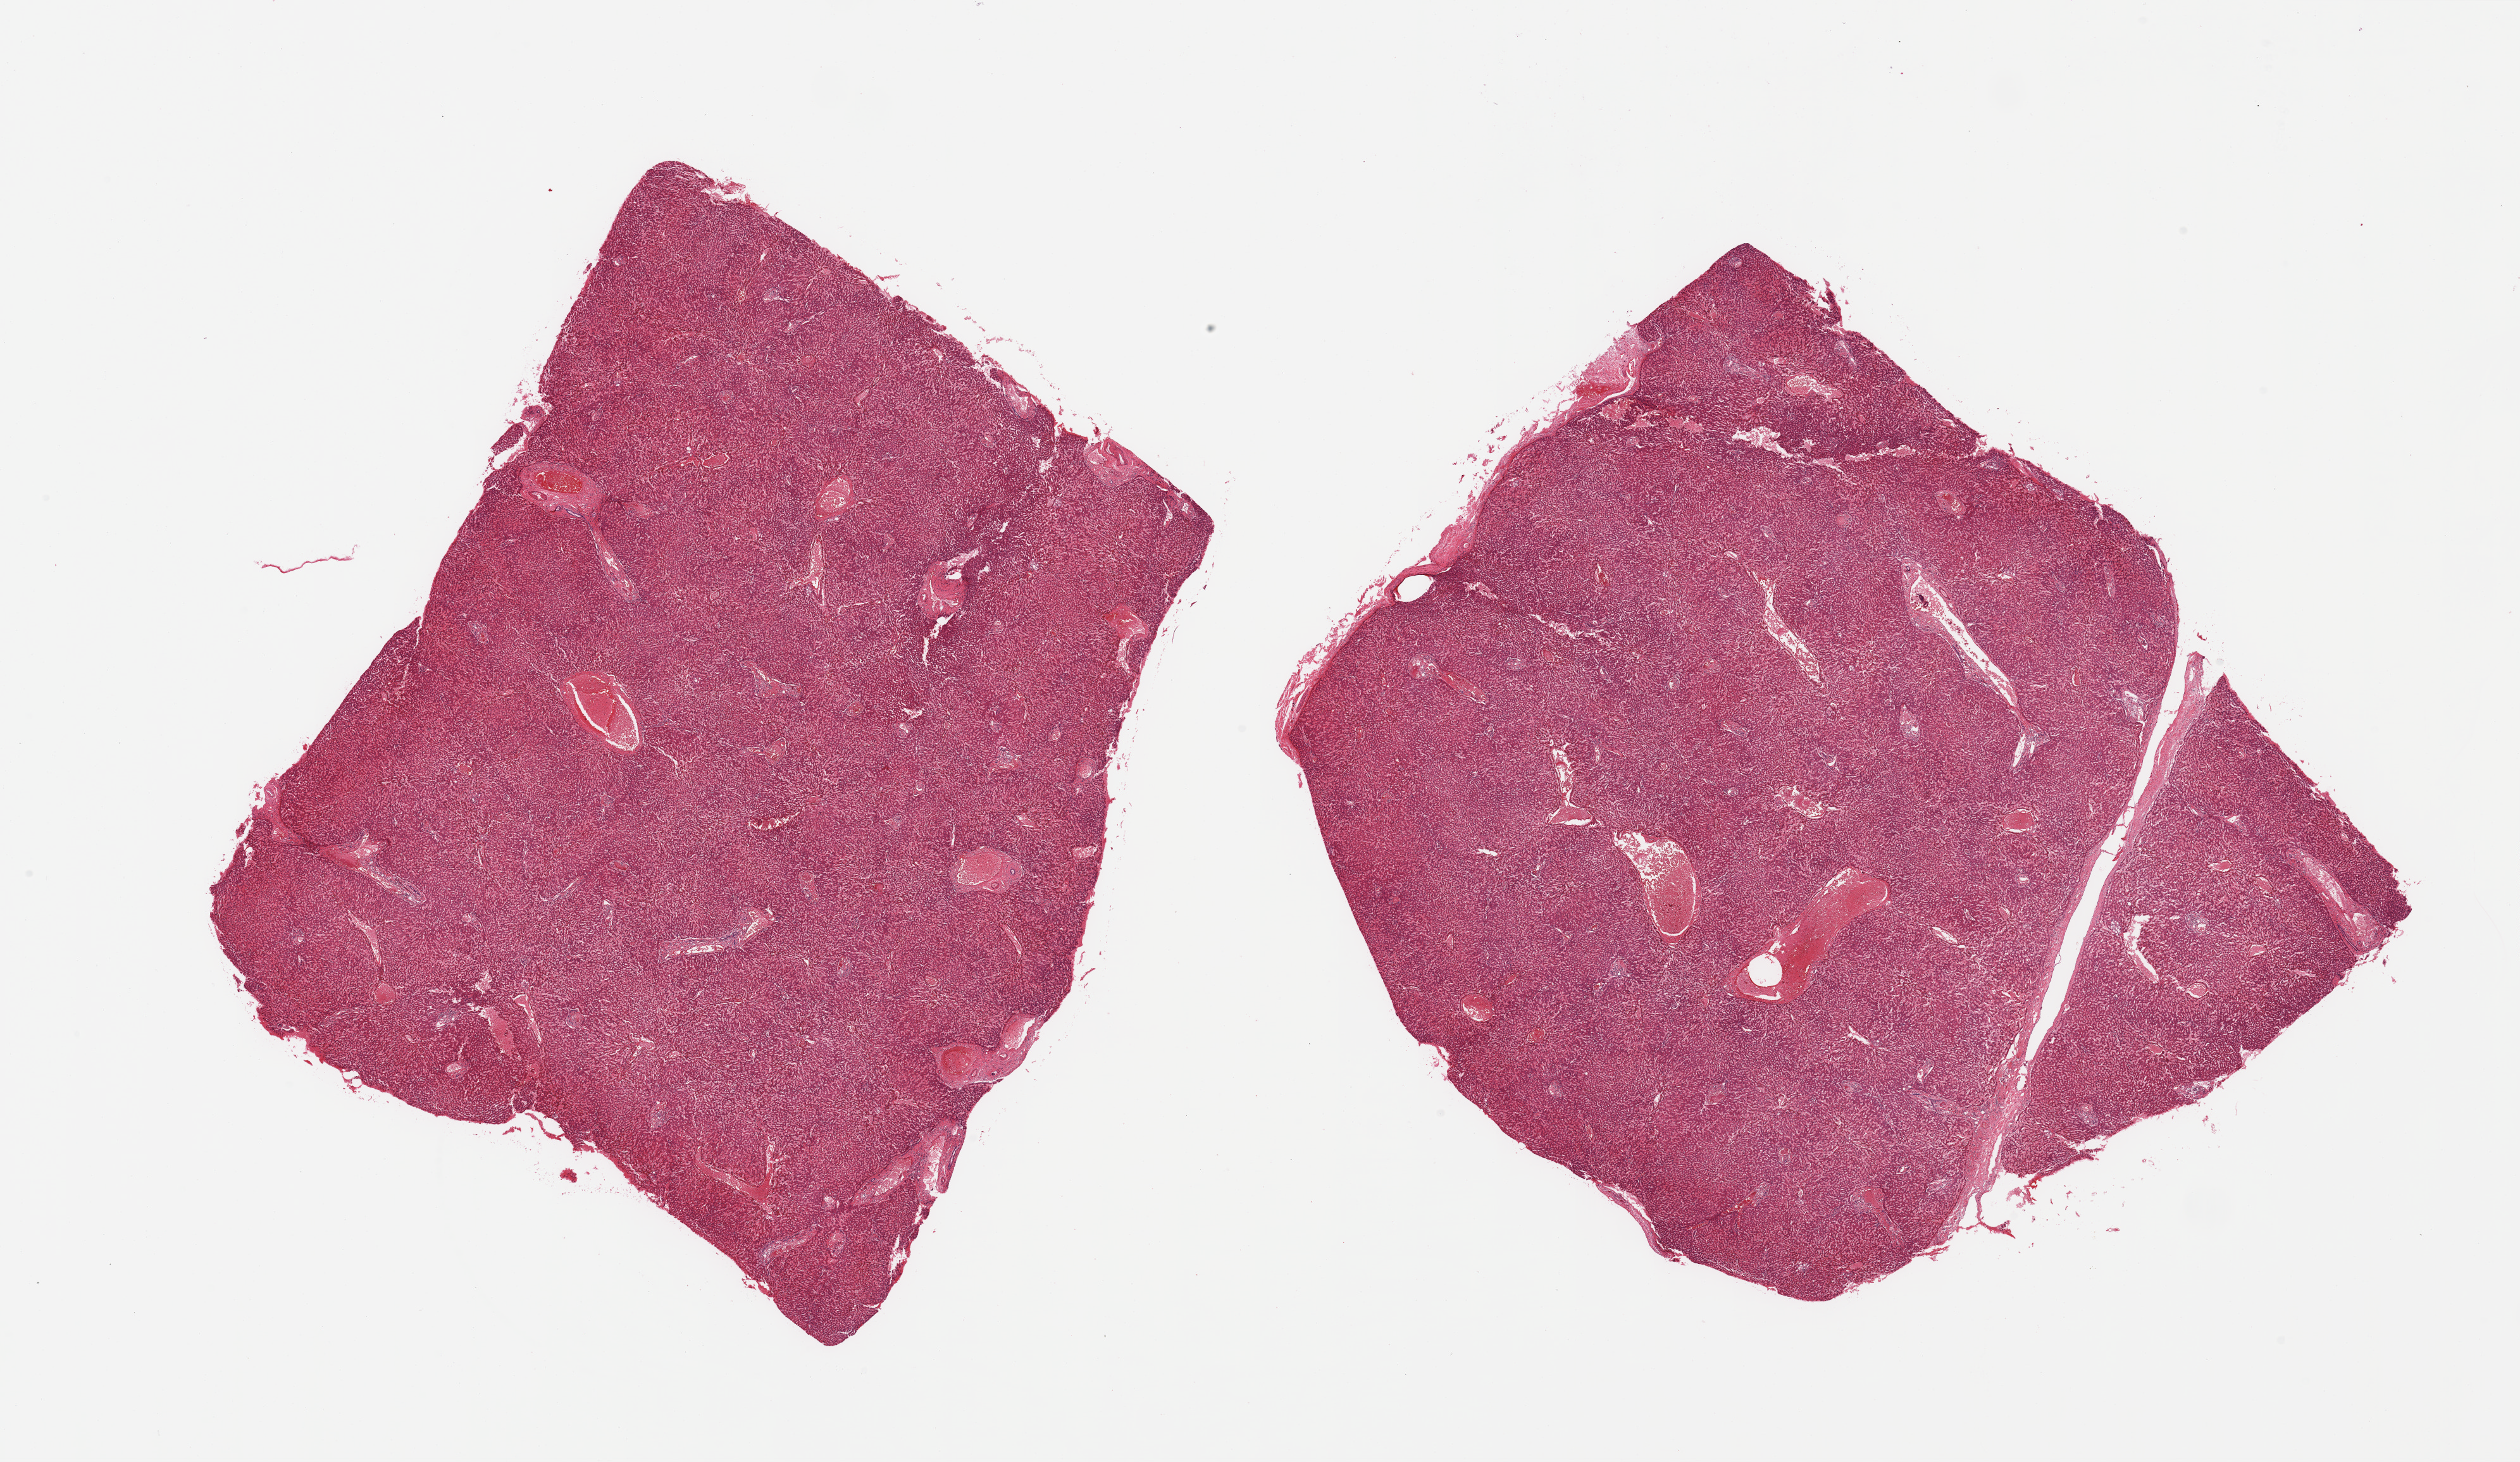
Haematoxylin and eosin whole-slide image — a low-resolution overview of the entire scanned area, about 31.5 x 18.3 mm, PAXgene-fixed, paraffin-embedded tissue, sampled site (target tissue): liver, donor tissue sample. Donor: male.
Pathologist's review note for this sample: 2 pieces; marked congestion.